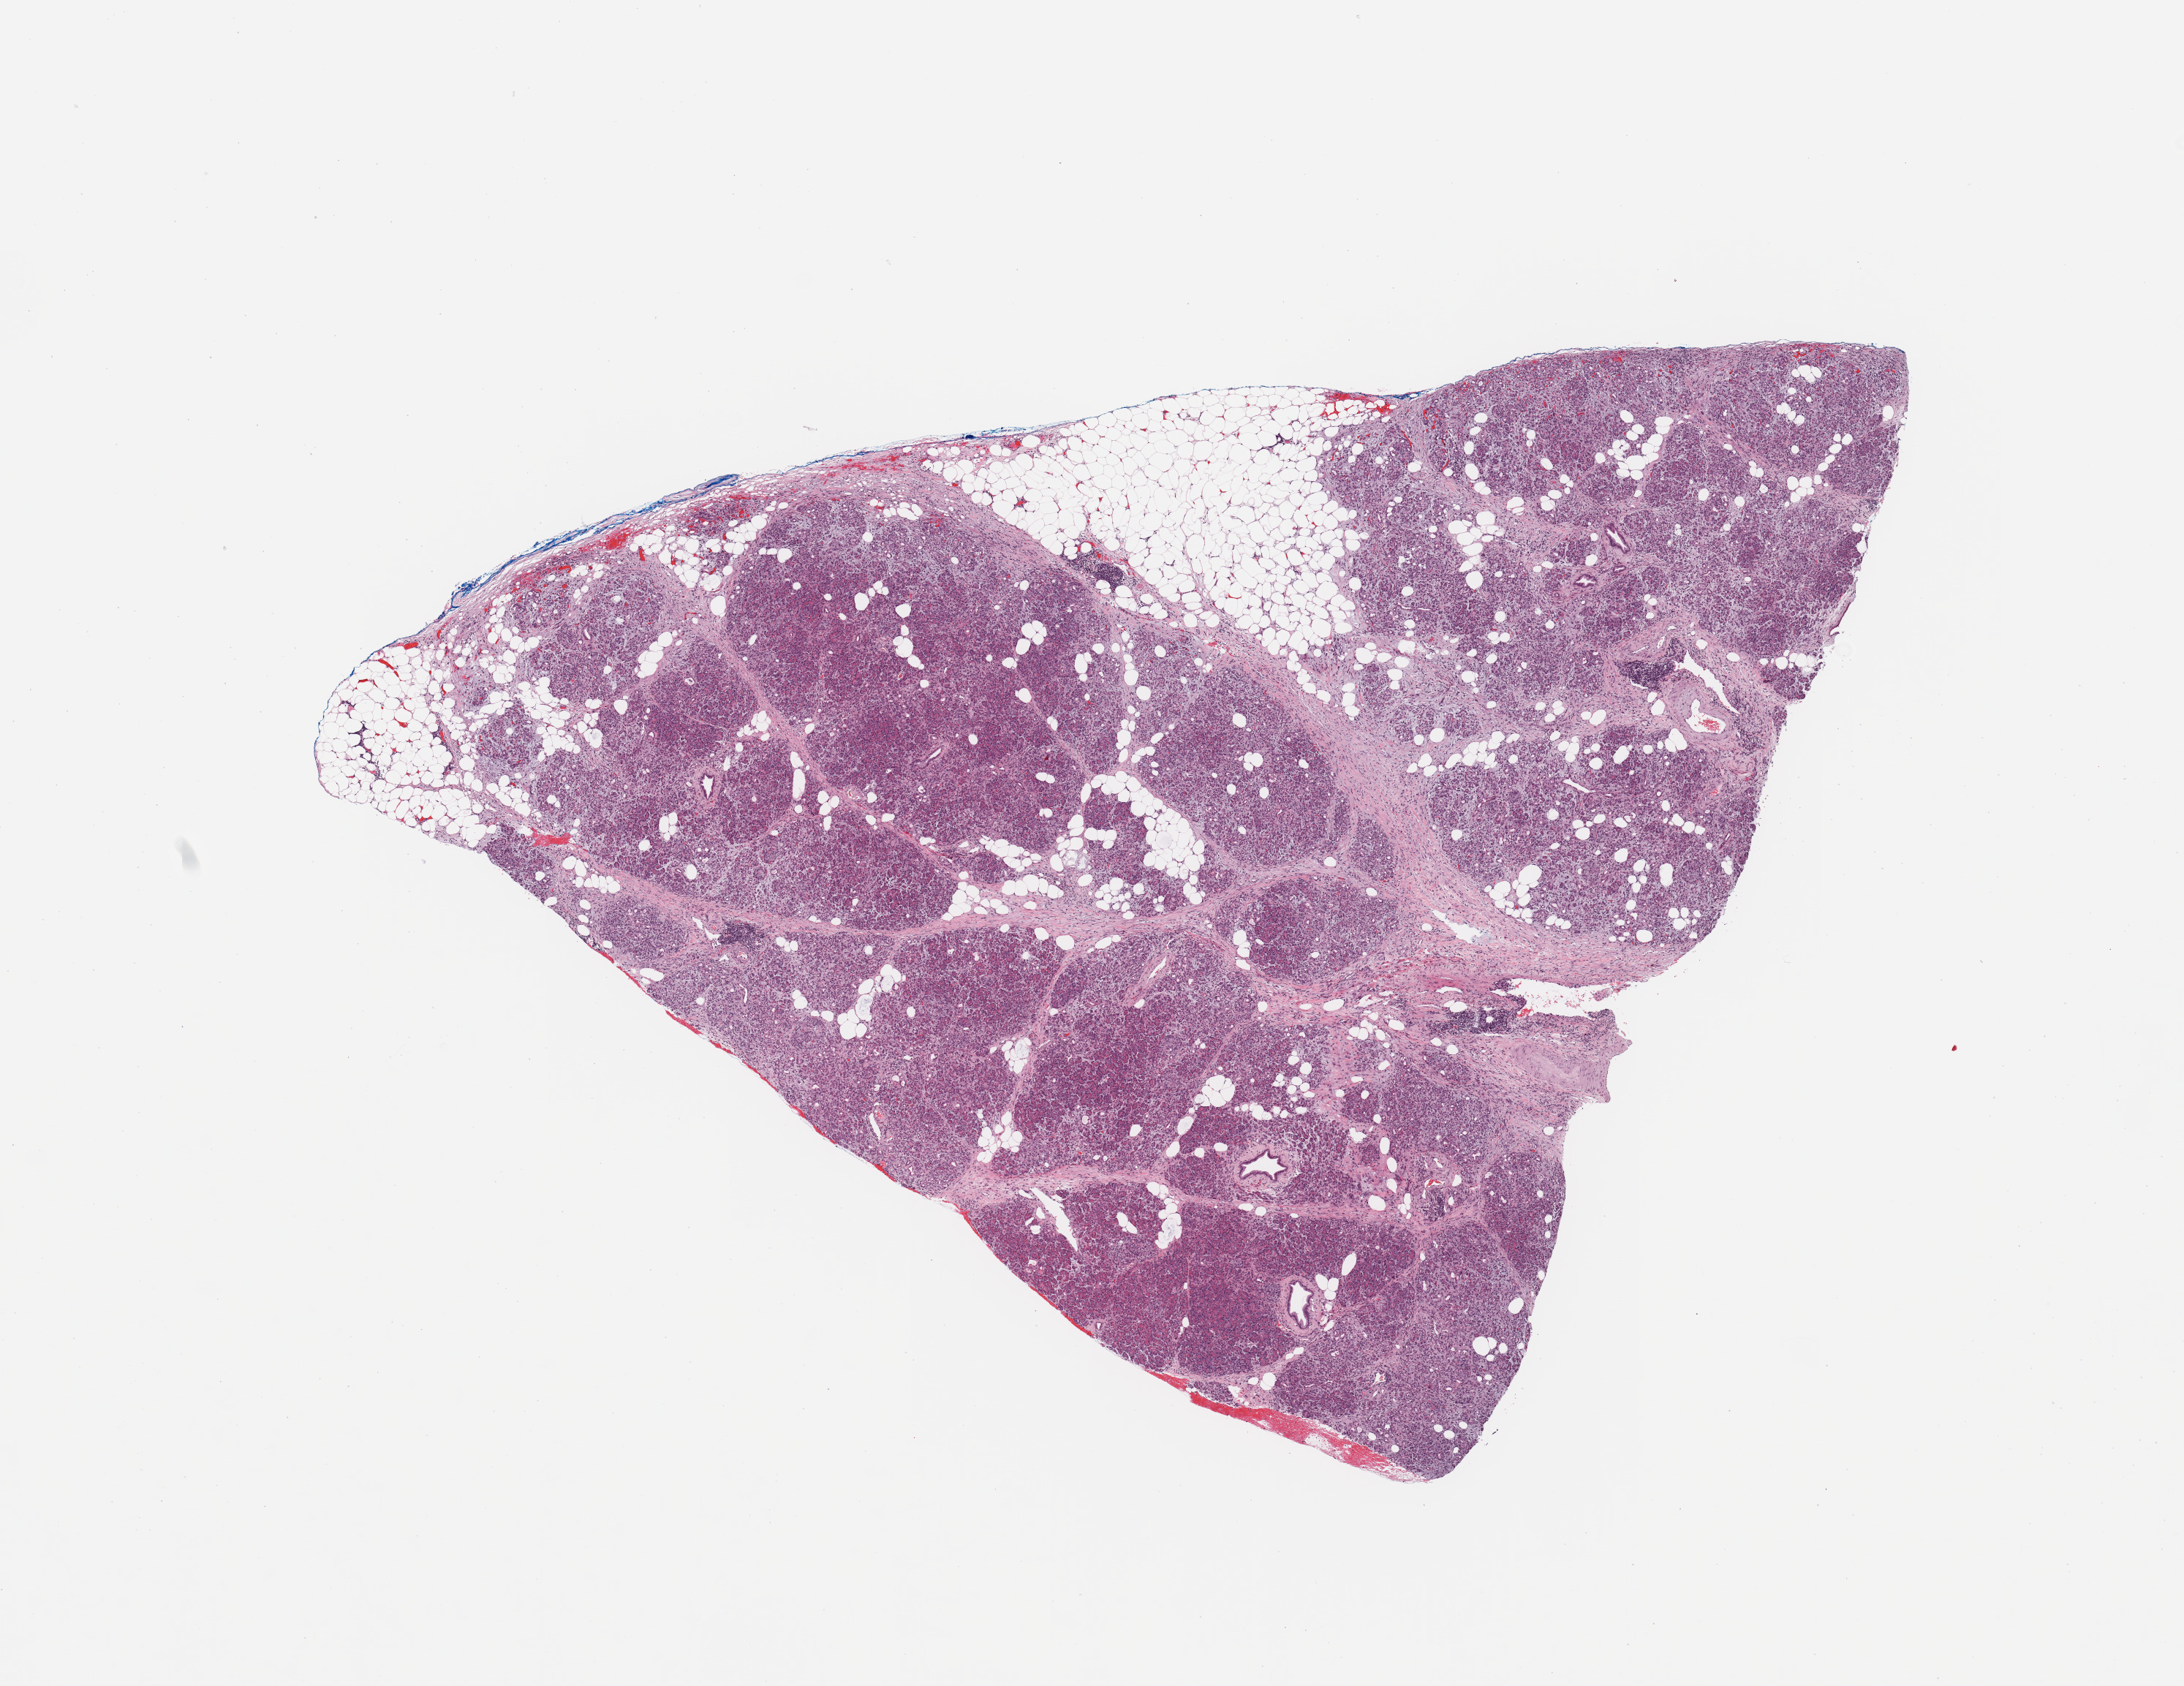
Hematoxylin and eosin (H&E) stained whole-slide image, whole scanned area (about 11.8 x 9.1 mm) shown as a low-resolution overview, normal (non-tumour) tissue sample, sampled site: pancreas. Patient: female, age 78 years.
This section: normal (non-tumour) tissue from the same patient. Patient diagnosis: Infiltrating duct carcinoma, NOS.